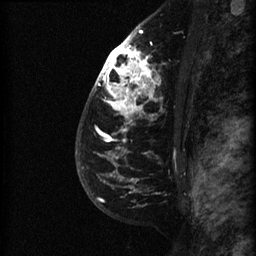
Breast MRI (dynamic contrast-enhanced), one sagittal slice. Dynamic contrast-enhanced series, image 2 of 3 at this slice position (ordered by acquisition). 1.5 T. TE 4.2 ms, TR 22.7 ms. 256 × 256 image matrix. Female patient, age 48 years. Case-level facts recorded for this patient, not image findings: setting: breast cancer imaged before/during neoadjuvant chemotherapy; receptor status: triple-negative.
Structures marked on this image (semi-automatically segmented with operator editing):
- analysis volume of interest (the breast-tissue region the enhancement analysis was run in; not a lesion): bounding box [x1, y1, x2, y2] px = [89, 27, 188, 180]
- tumour enhancement mask (voxels above the 90 % enhancement threshold inside the analysis volume of interest): [97, 30, 153, 180]